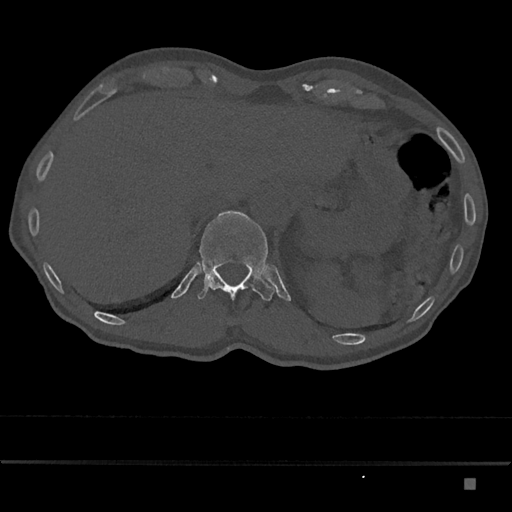
CT including the spine, one axial slice. Slice 617 of 797 in the series (ordered by position). Reconstruction kernel Br40s/3. 120 kVp. Bone window (W 1800 / L 400 HU). 512 × 512 image matrix, field of view 390 × 390 mm. Male patient, age 72 years. From the clinical record (not read from this slice): primary cancer: prostate.
Structures marked on this image (semi-automatic segmentation, software-assisted and operator-edited):
- T12 vertebra: bounding box (x1, y1, x2, y2) in pixels: (197, 211, 275, 301)